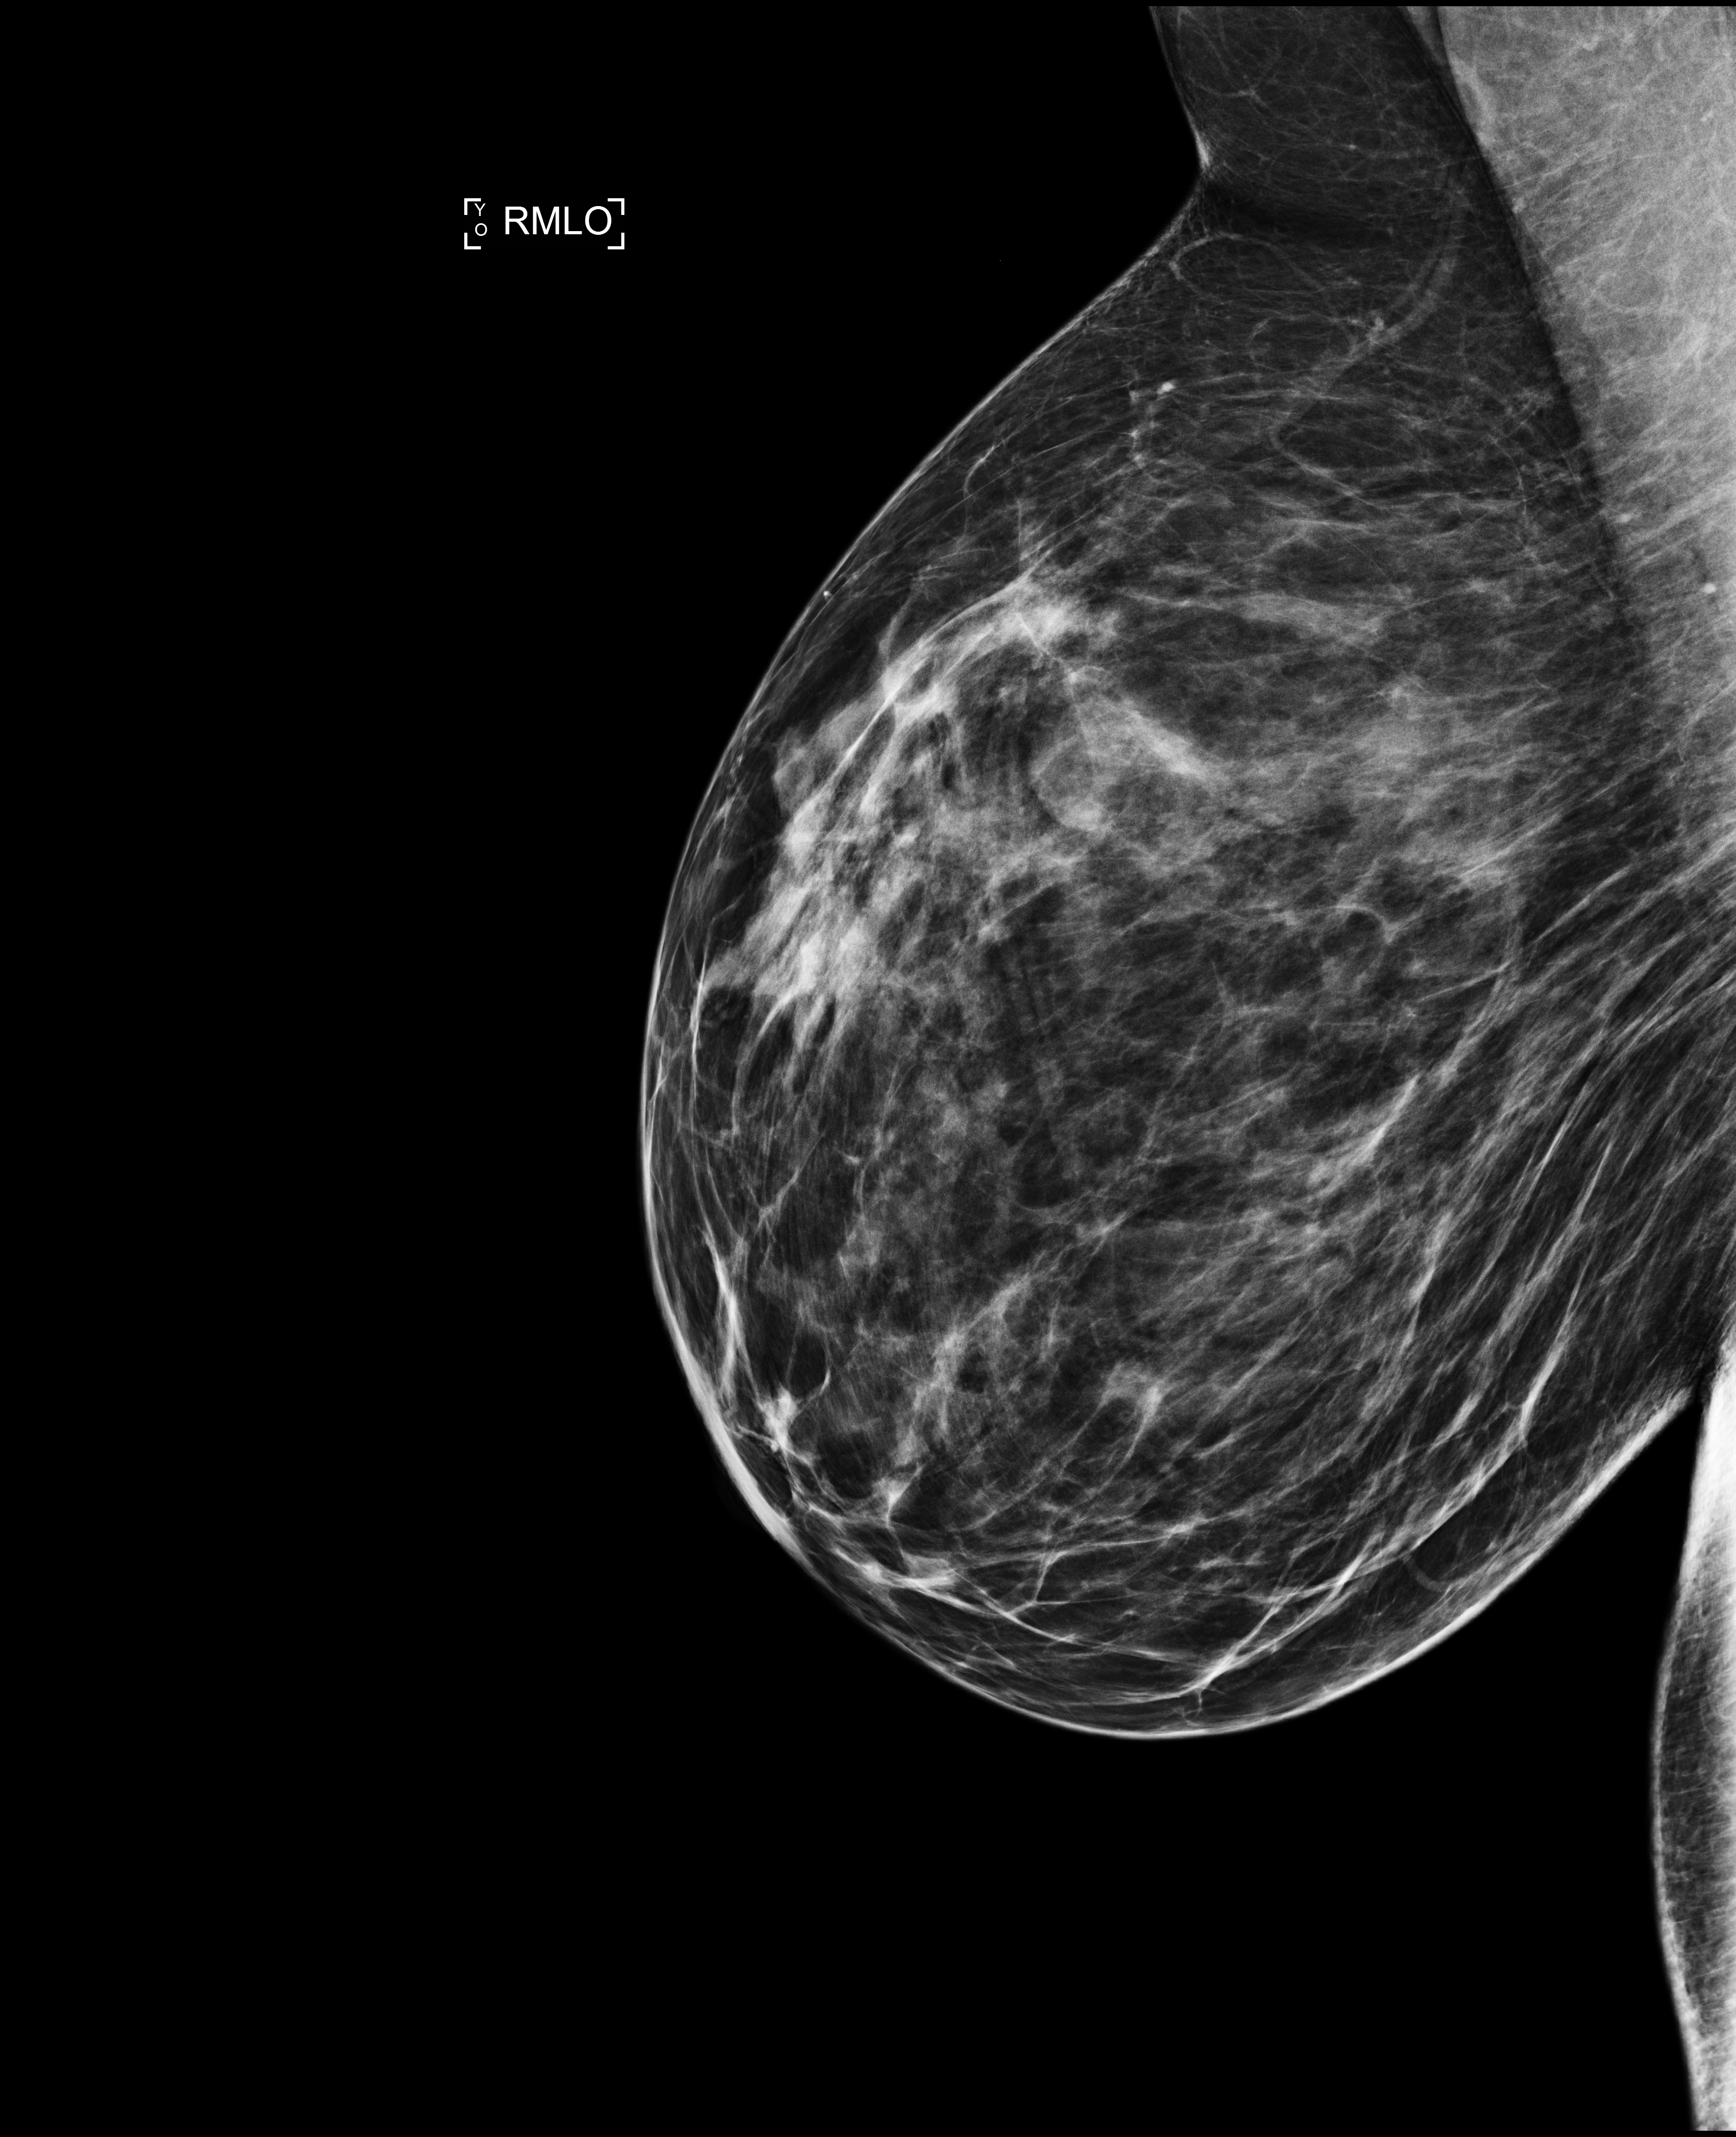
Screening examination; system: Selenia Dimensions. Patient aged 43 years (female).
Image type: full-field digital mammogram. Breast: right. Projection: medio-lateral oblique projection.